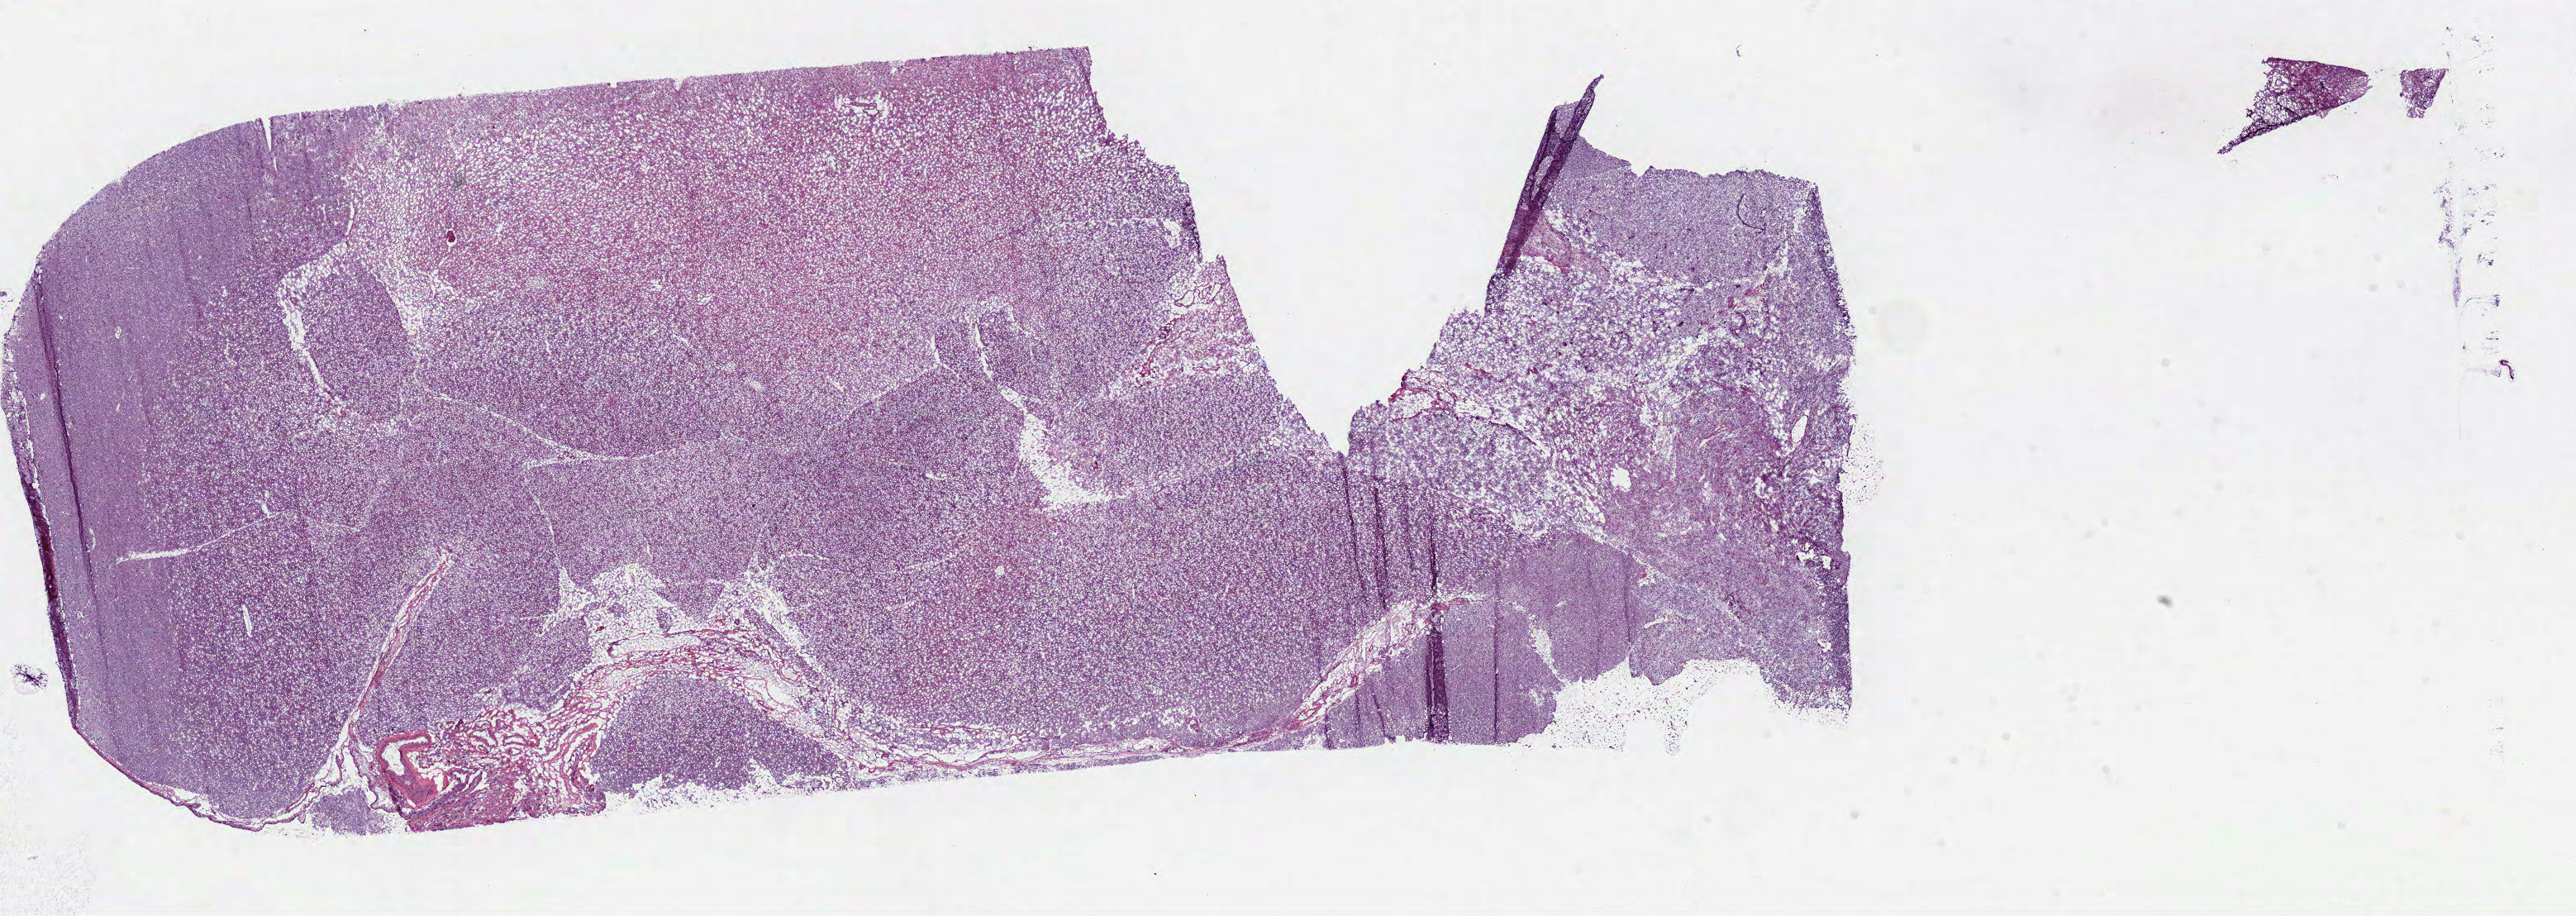
Digitized H&E tissue section (whole slide) — low-resolution overview of the scanned area, about 25.1 x 8.9 mm (acquisition: 40x scan), frozen section, sample: primary tumour, brain. Patient: male, age at initial diagnosis 35 years. Histologic grade: G3 (poorly differentiated).
Pathologic diagnosis: Oligodendroglioma, anaplastic (cerebrum).